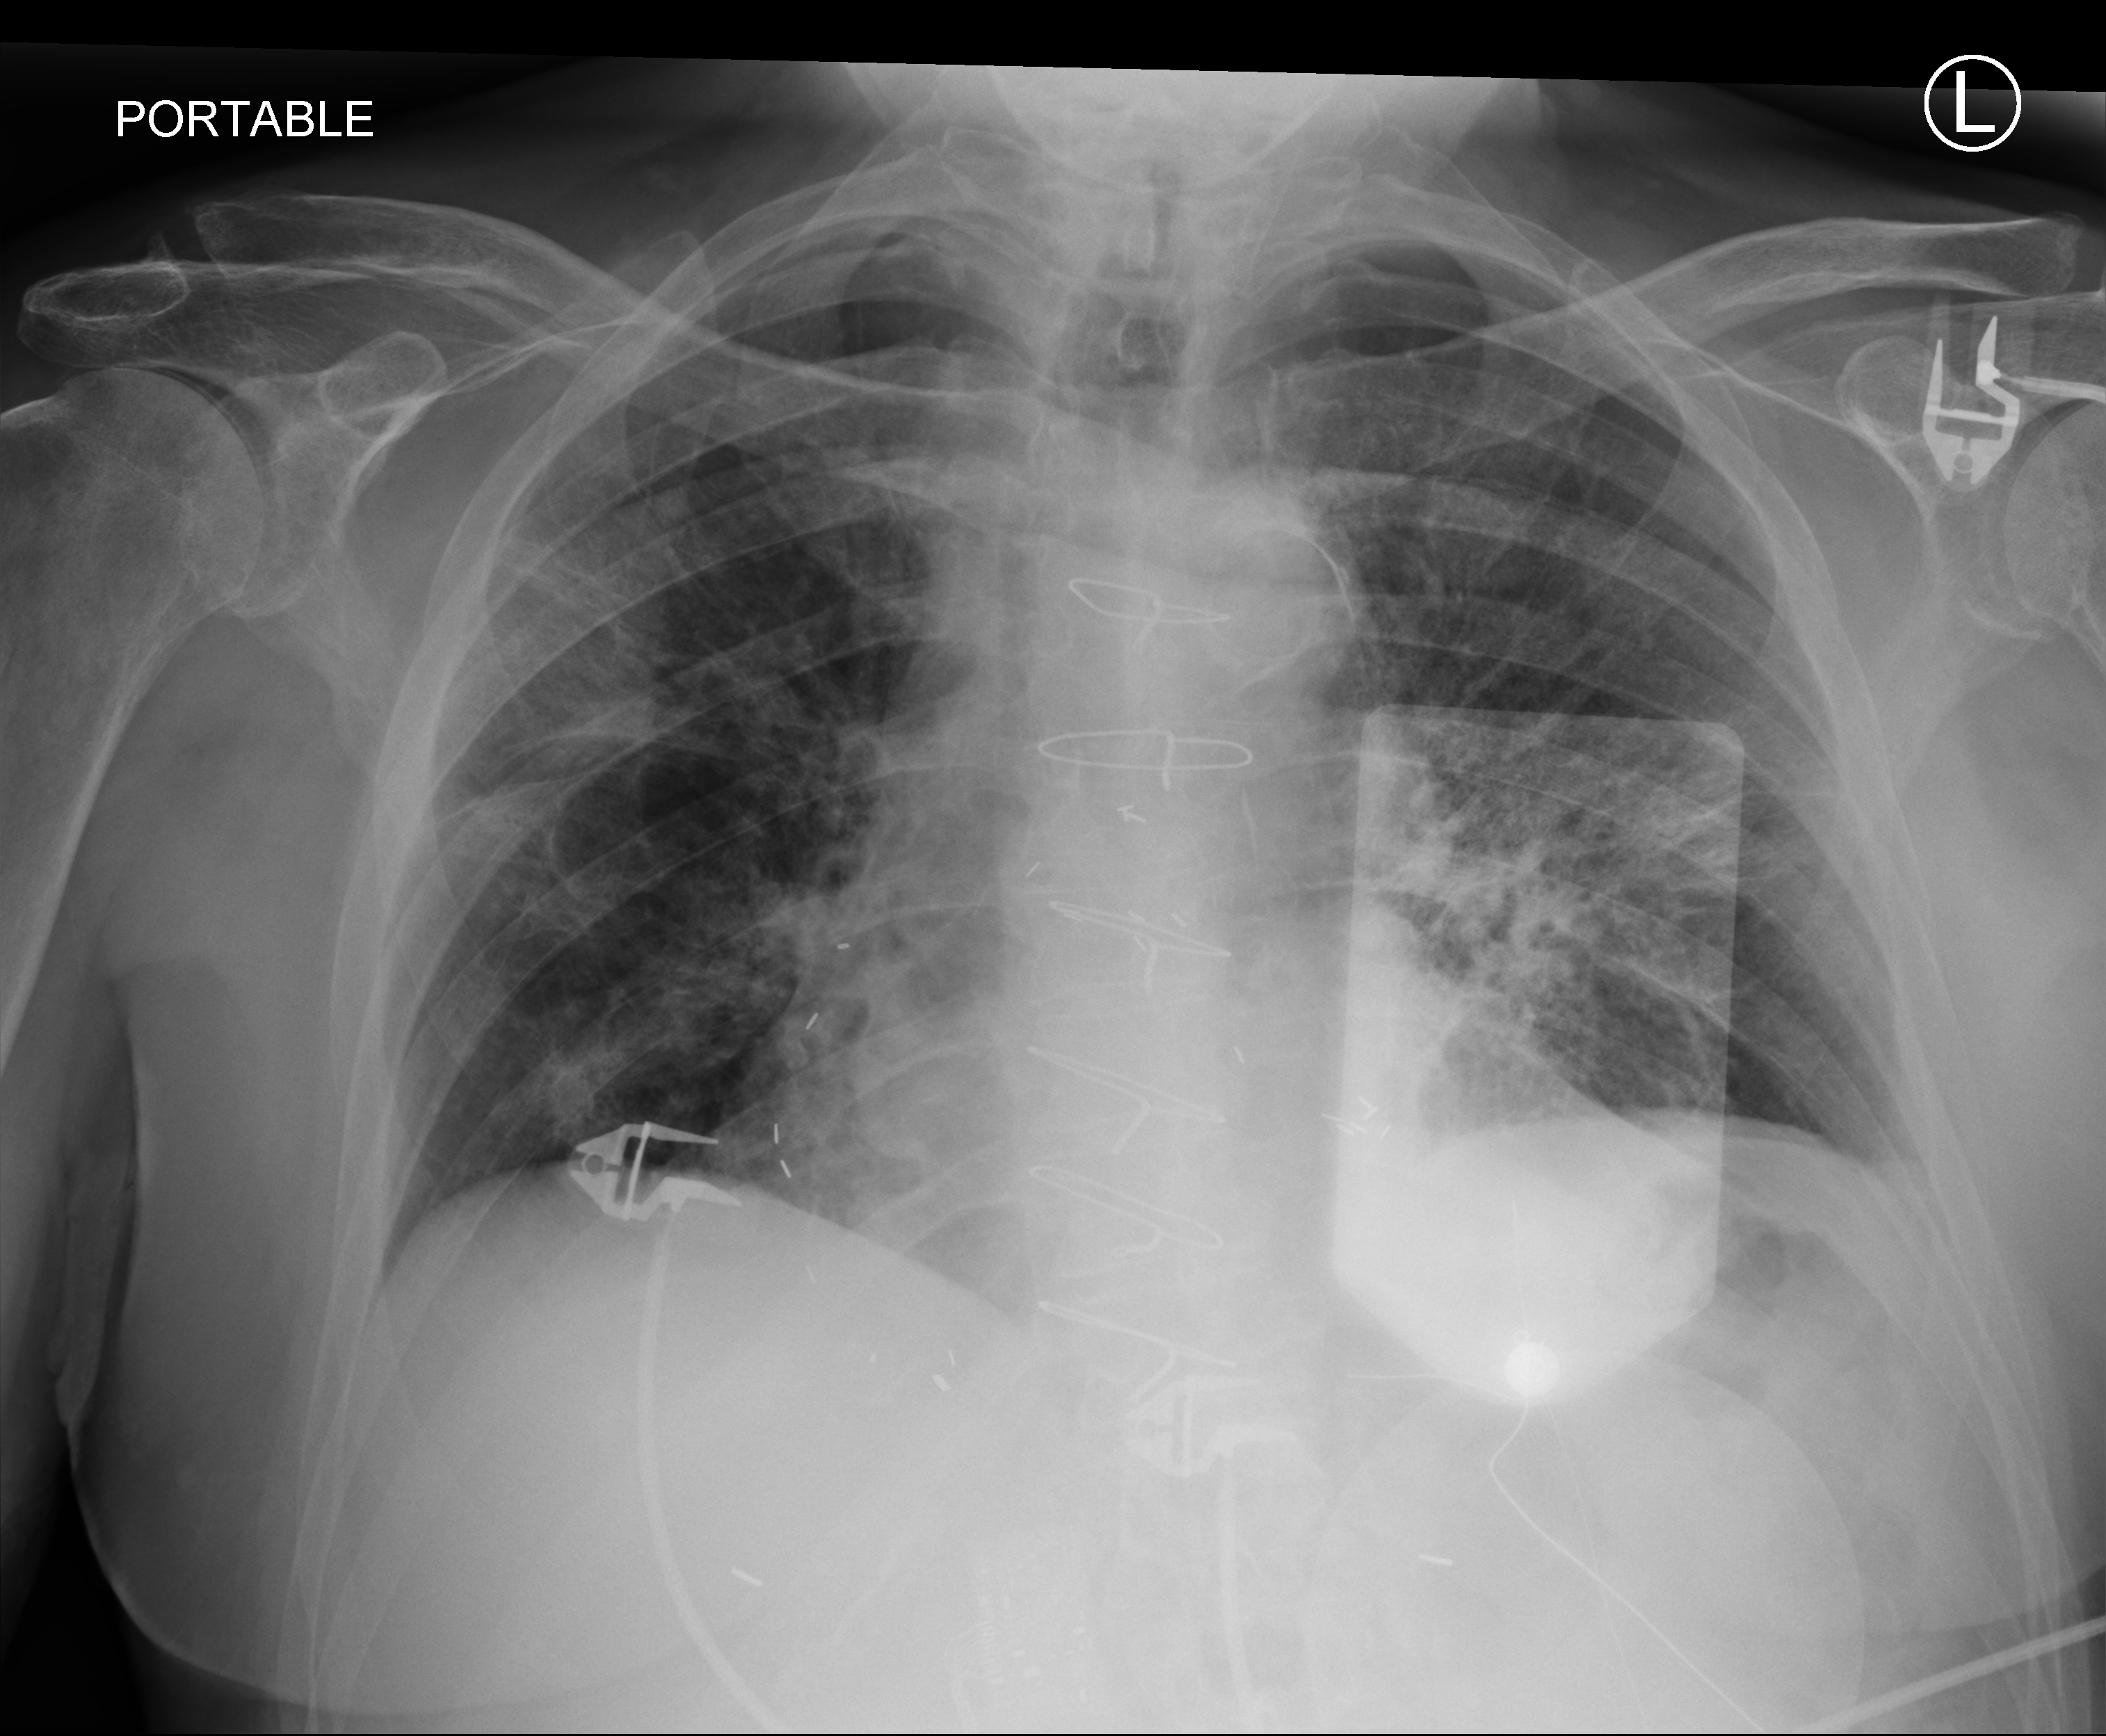
Portable chest radiograph, anteroposterior (AP) projection. Male patient hospitalised with COVID-19, age 75–90 years.
Admission-level facts for this patient (not findings on this image; timing relative to this image not recorded):
- smoking status (admission record): never